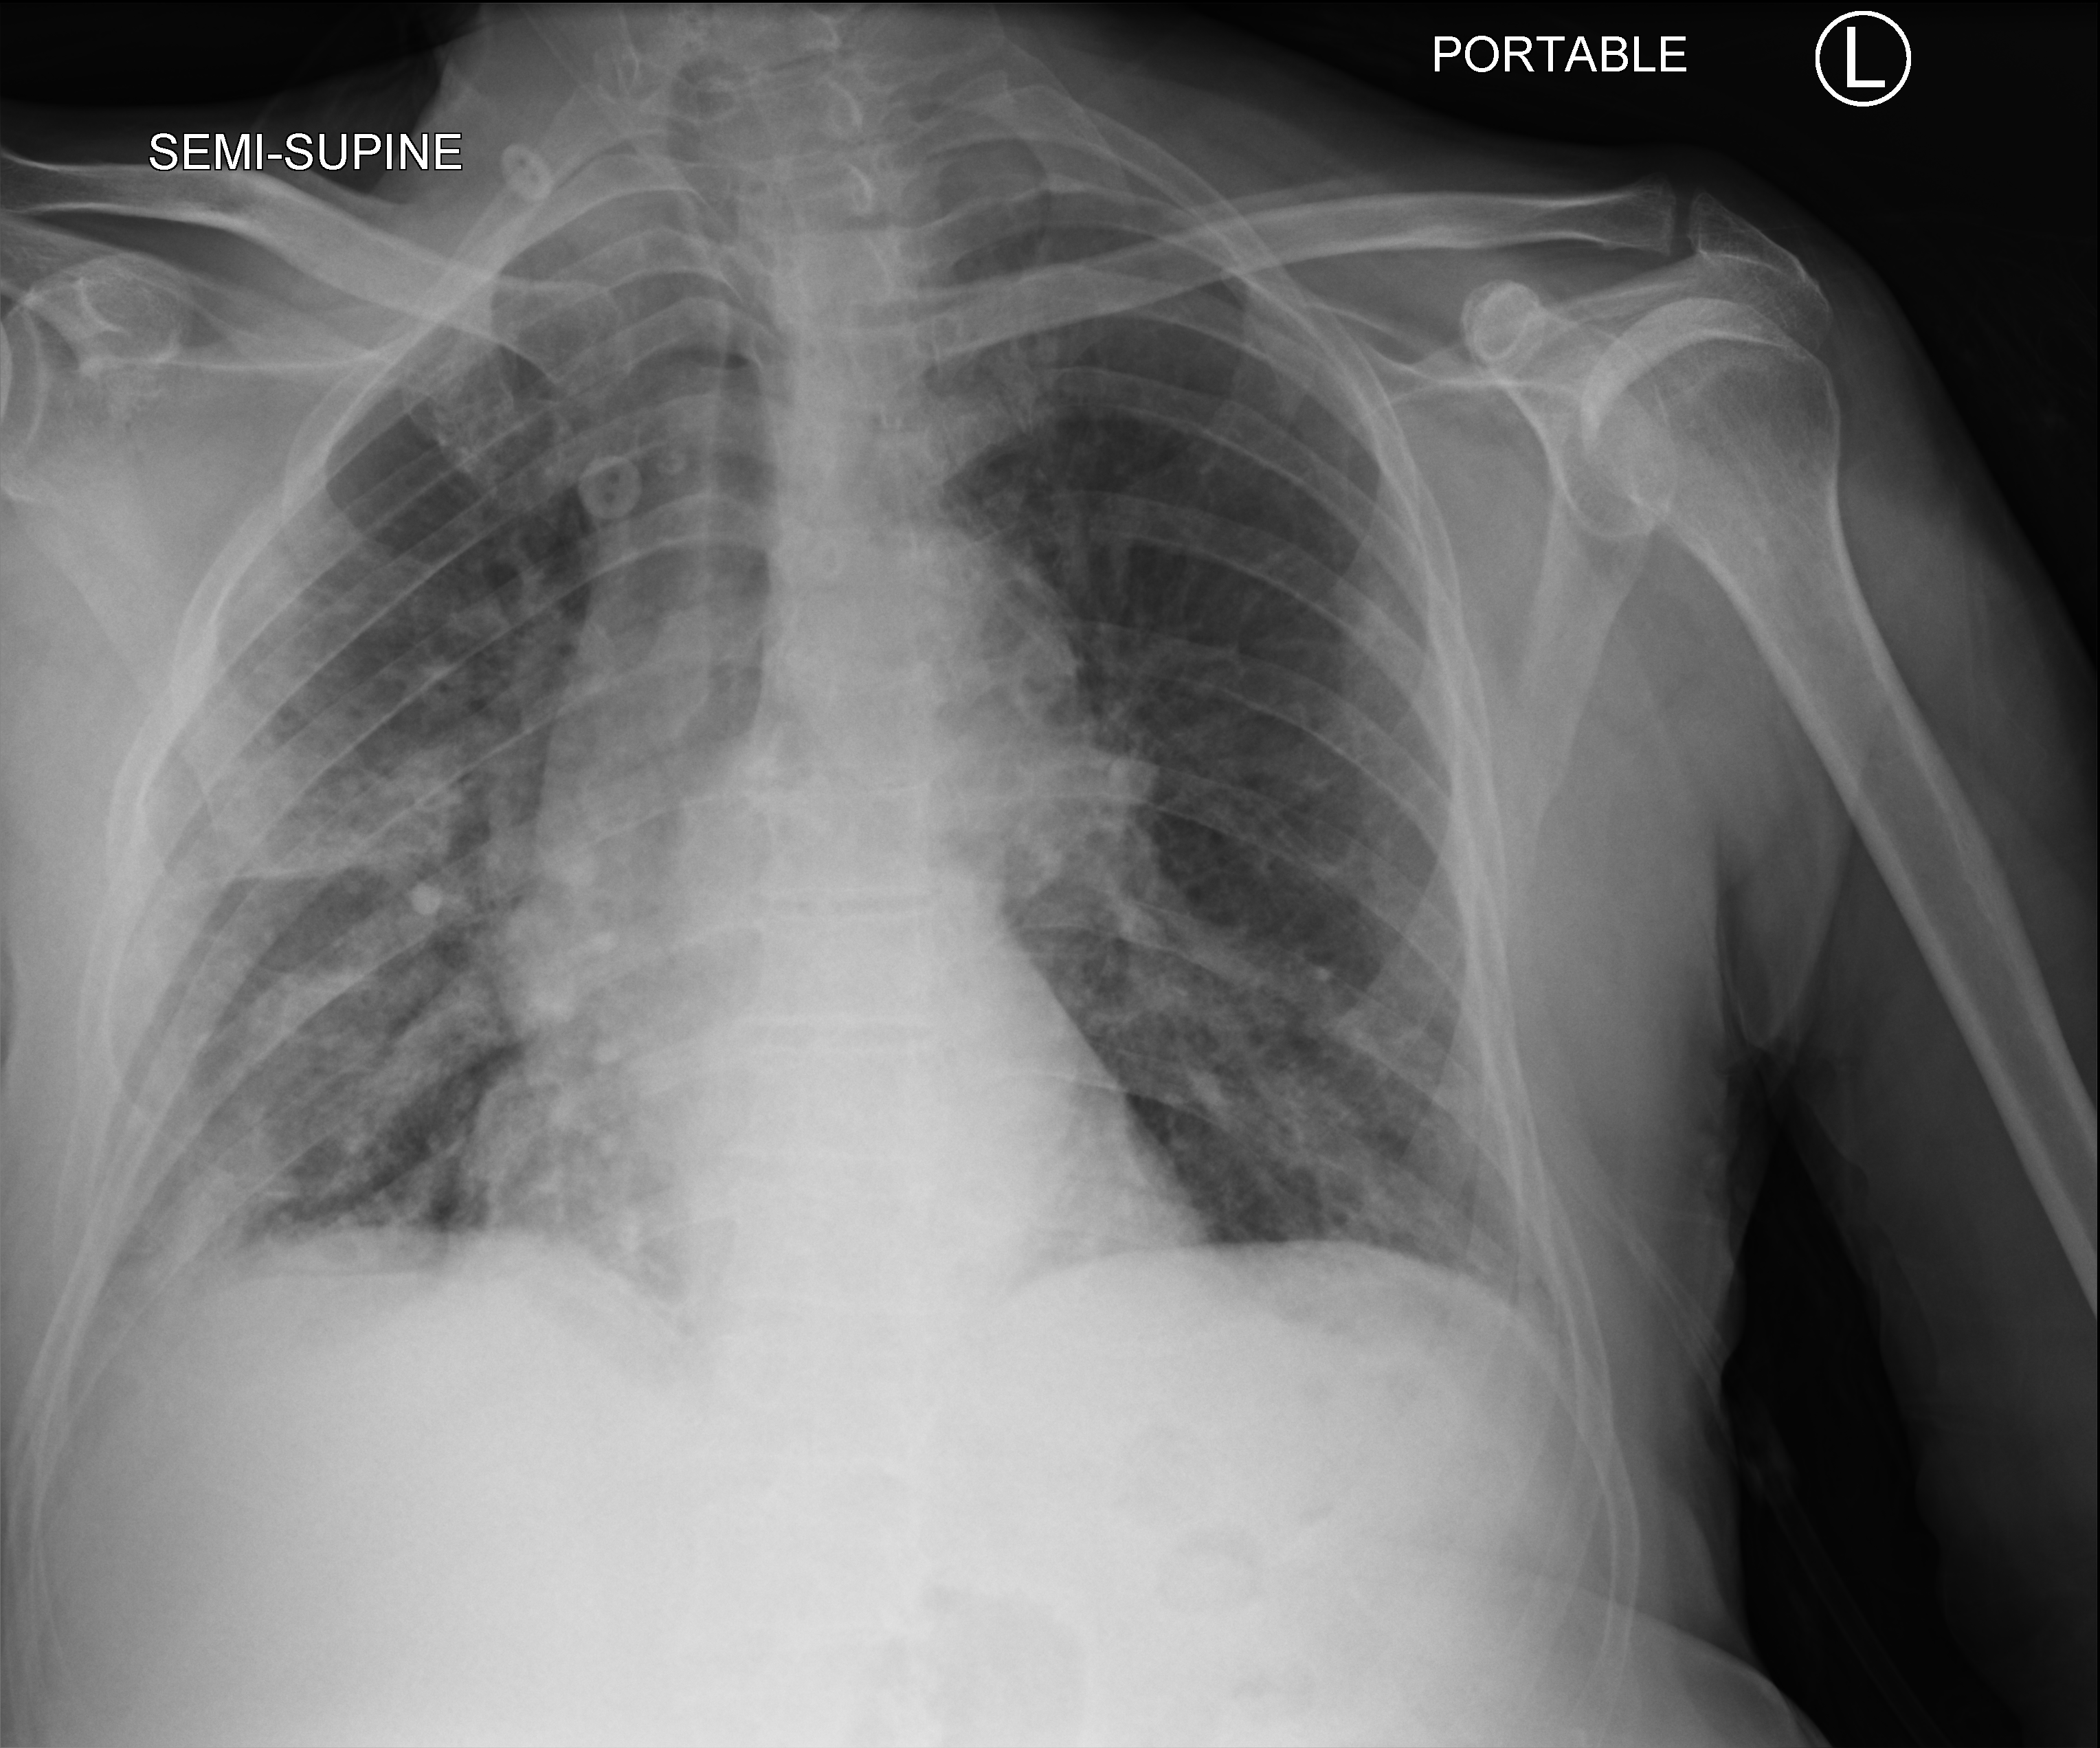
Portable chest radiograph; anteroposterior (AP) projection. Male patient hospitalised with COVID-19, age 75–90 years.
From the hospital-stay record, not from the radiograph (when in the stay this image was taken is not recorded): mechanically ventilated during this hospital stay: yes.